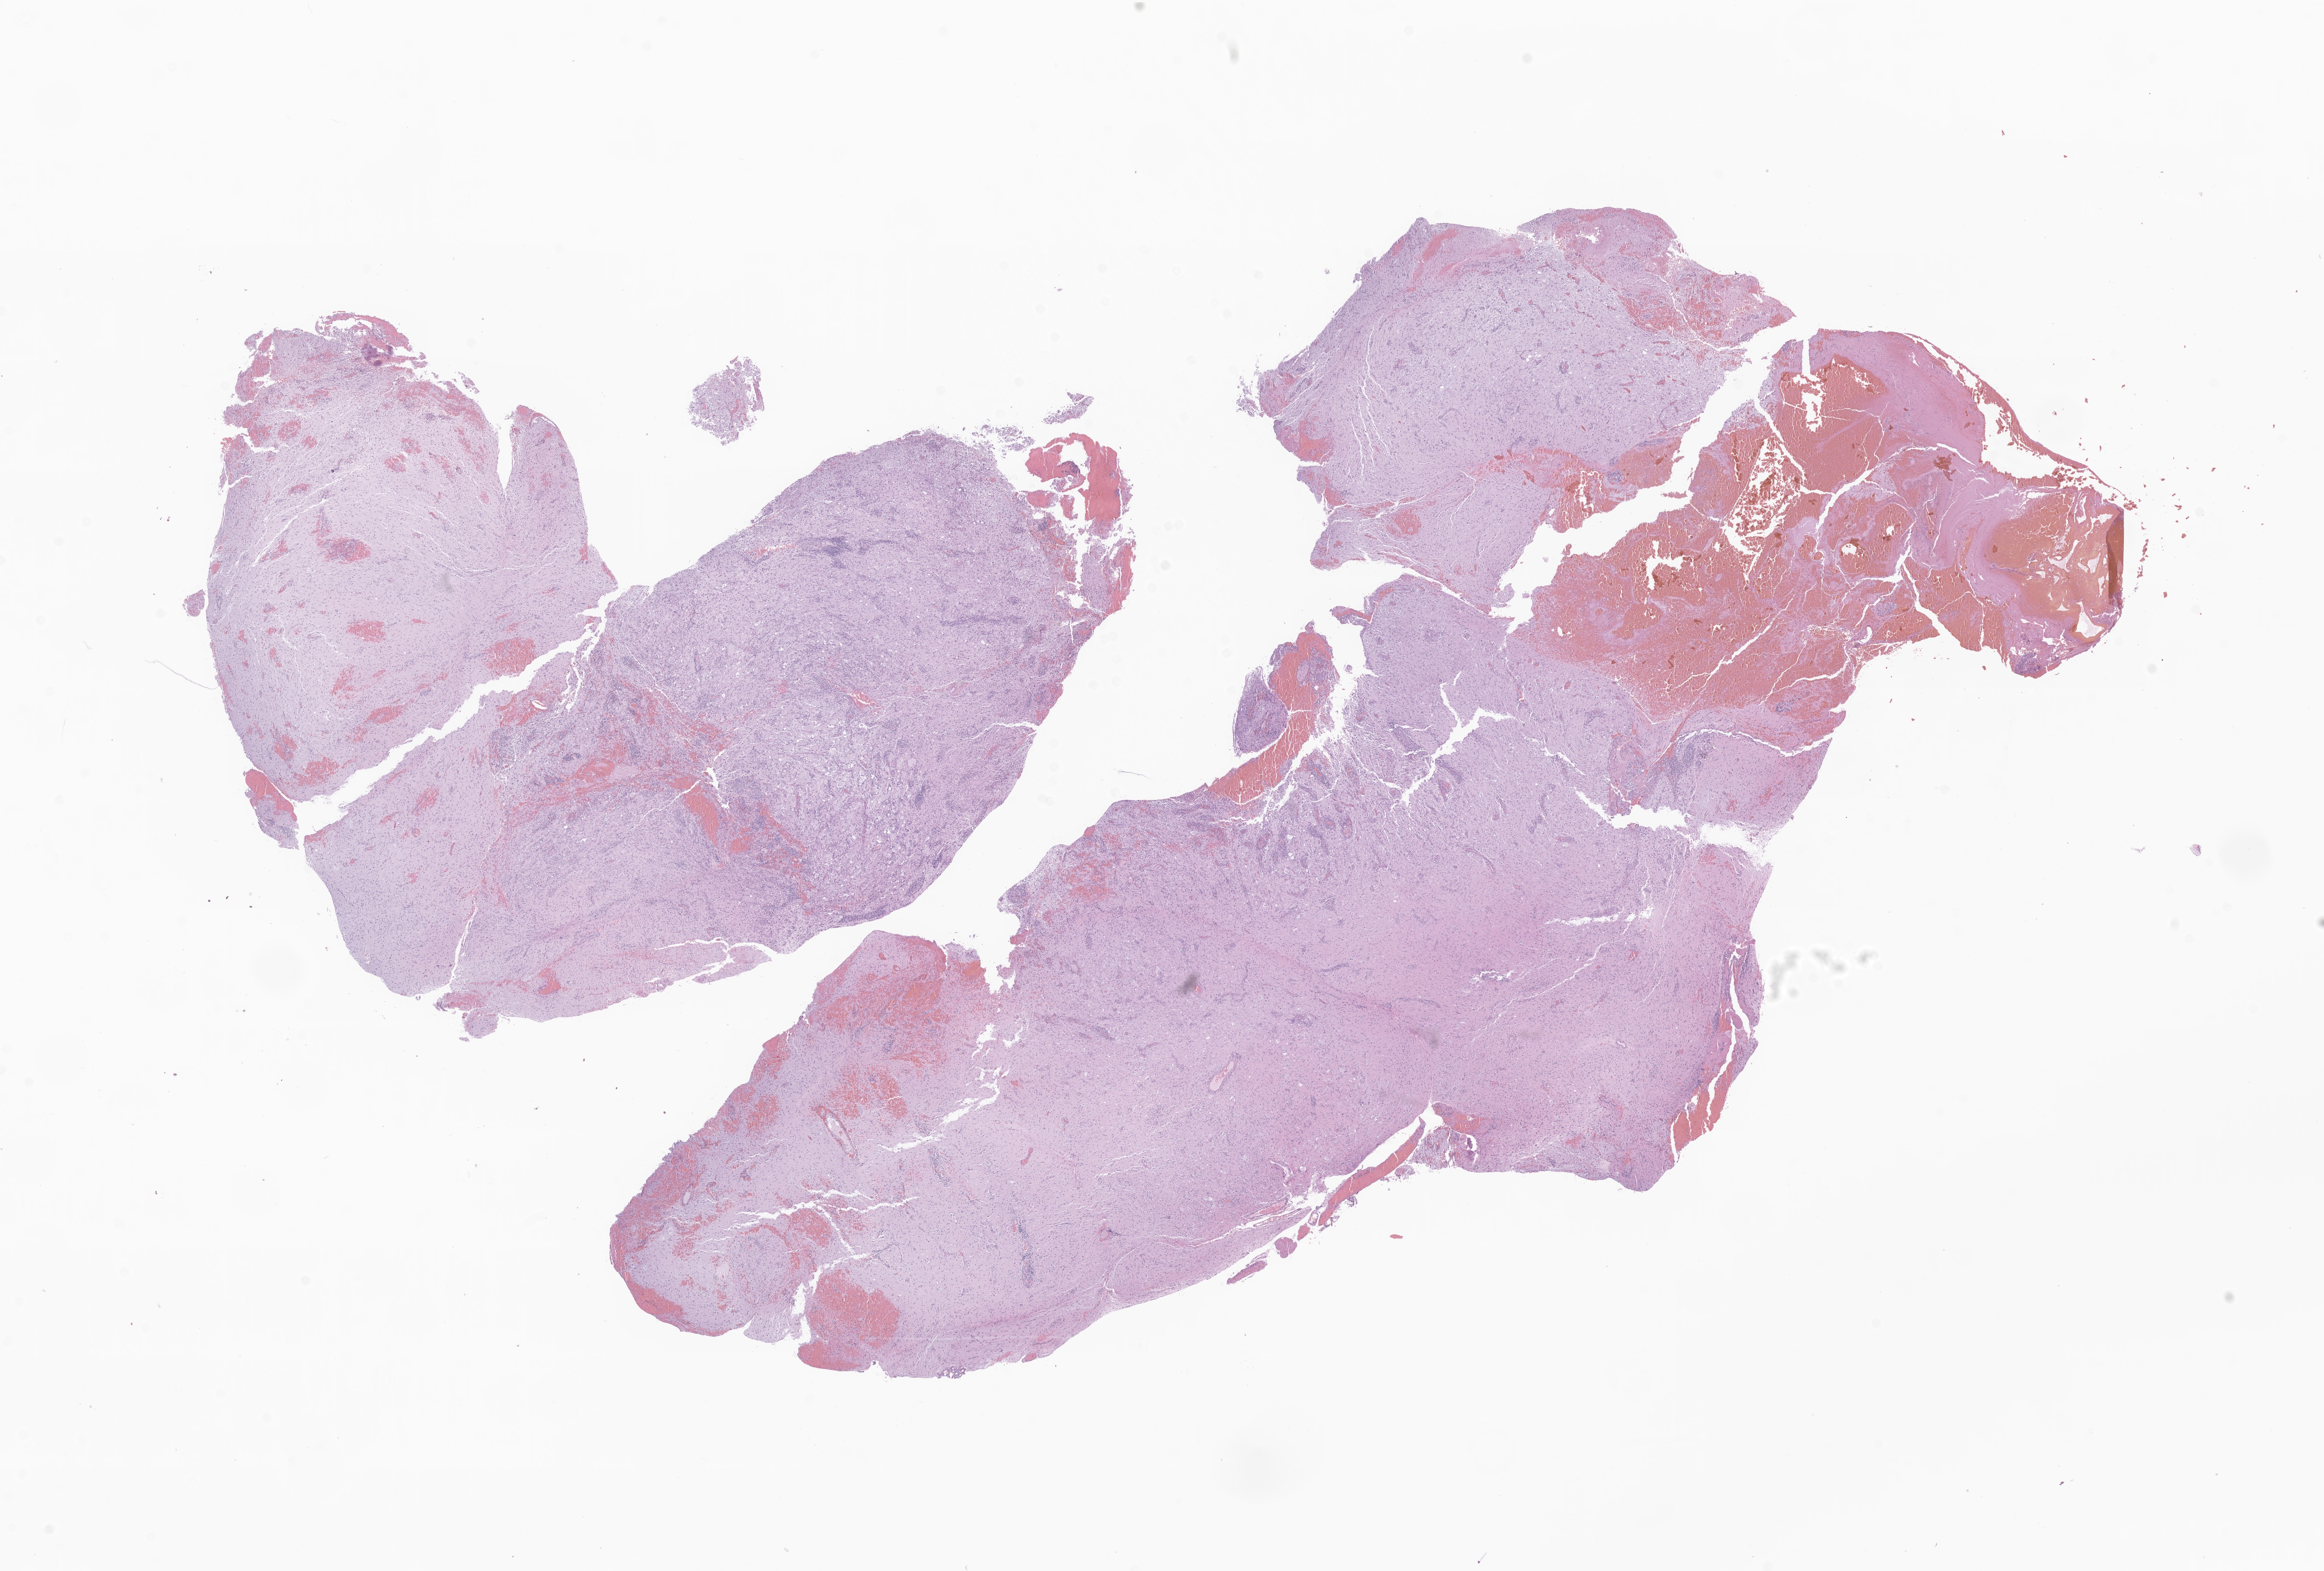
Whole-slide image, H&E stain of tumor tissue from the cerebral ventricle, low-resolution overview of the scanned area, about 22.4 x 15.2 mm, formalin-fixed, paraffin-embedded (FFPE) tissue. Female patient, age 123 months (10 years 3 months).
Diagnosis (ICD-O-3 morphology term): Ganglioneuroma.